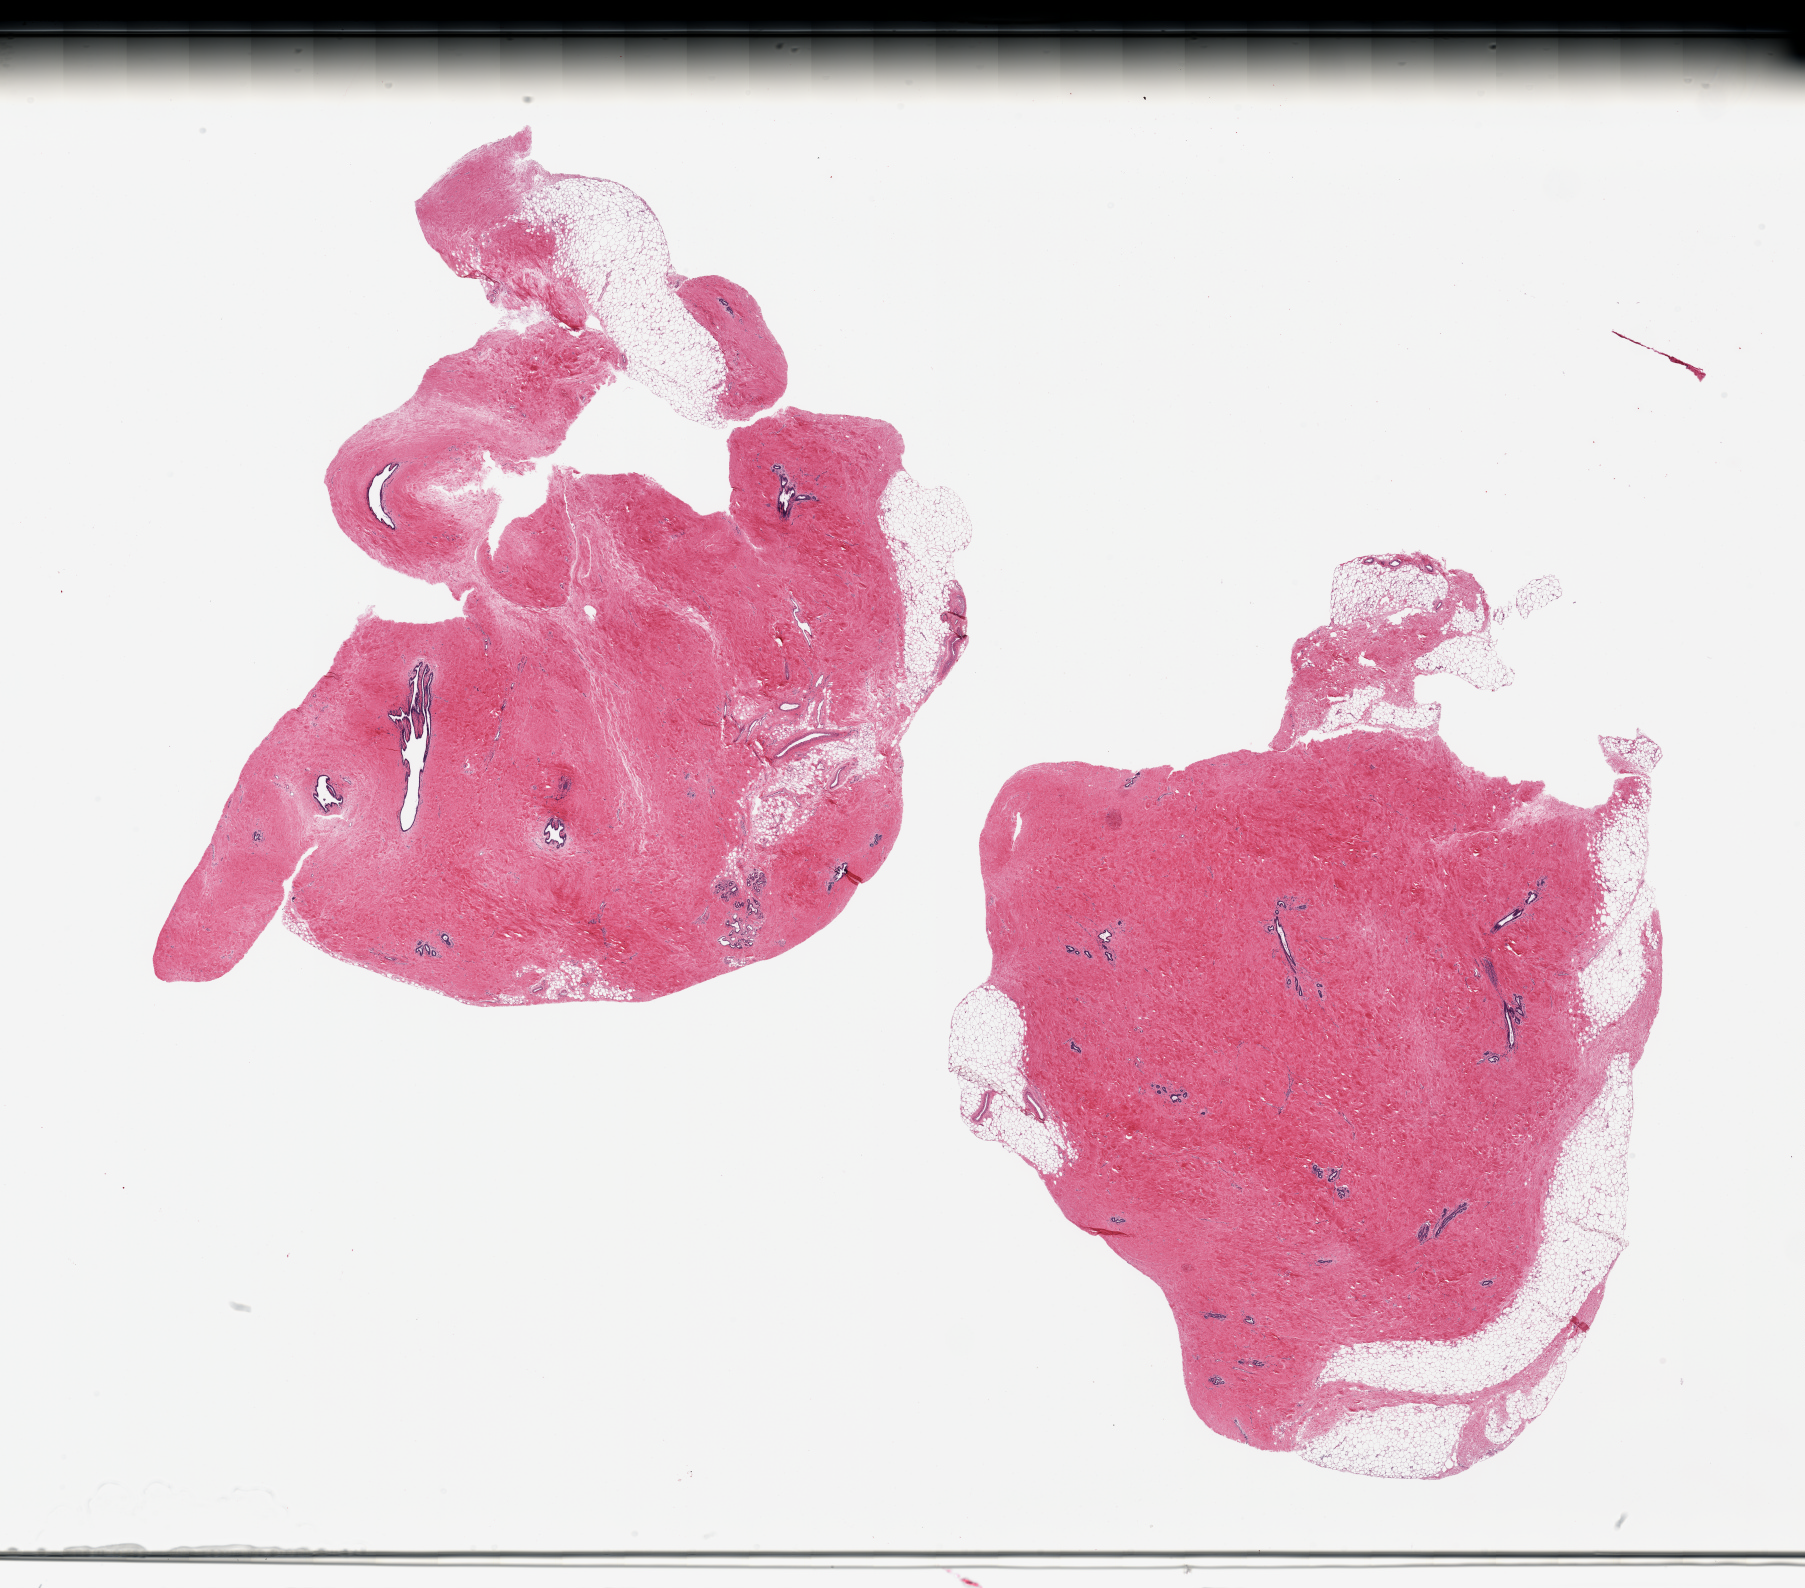
Digitized hematoxylin and eosin (H&E)-stained section, brightfield, whole scanned area (about 28.5 x 25.1 mm, from a 20x scan) shown as a low-resolution overview, PAXgene-fixed paraffin-embedded (PFPE) section, sampled site (target tissue): breast, tissue donor sample. Donor: male.
* review note (as recorded): 2 pieces; gynecomastoid stromal and ductal hyperplasia and adipose tissue